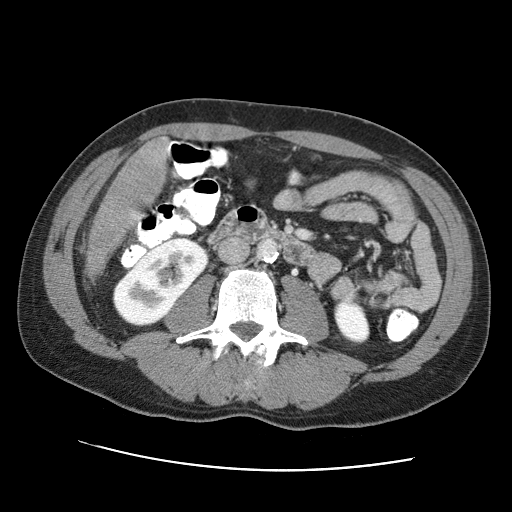
Contrast-enhanced abdominal CT (liver protocol), one axial slice; position 11 of 95 along the scan axis; one of 2 acquisitions stored at this slice position; soft-tissue window (W 400 / L 40 HU); 2.5 mm slice thickness; 512 × 512 image matrix, field of view 360 × 360 mm. From the clinical record (not read from this slice): diagnosis: hepatocellular carcinoma (patient treated with transarterial chemoembolisation; whether this scan precedes or follows treatment is not stated here); TNM stage (as recorded): Stage-IVA; Child-Pugh class: A; tumour differentiation: moderately differentiated; tumour nodularity: multinodular.
Outlined on this slice (semi-automatically segmented with operator editing):
- liver parenchyma outside the tumour (the mass and vessels are separate outlines, so this box may not span the whole liver): box from (x=137, y=143) to (x=170, y=222) px
- mass: (x=83, y=136)–(x=168, y=282)
- liver vessels: (x=167, y=147)–(x=170, y=153)